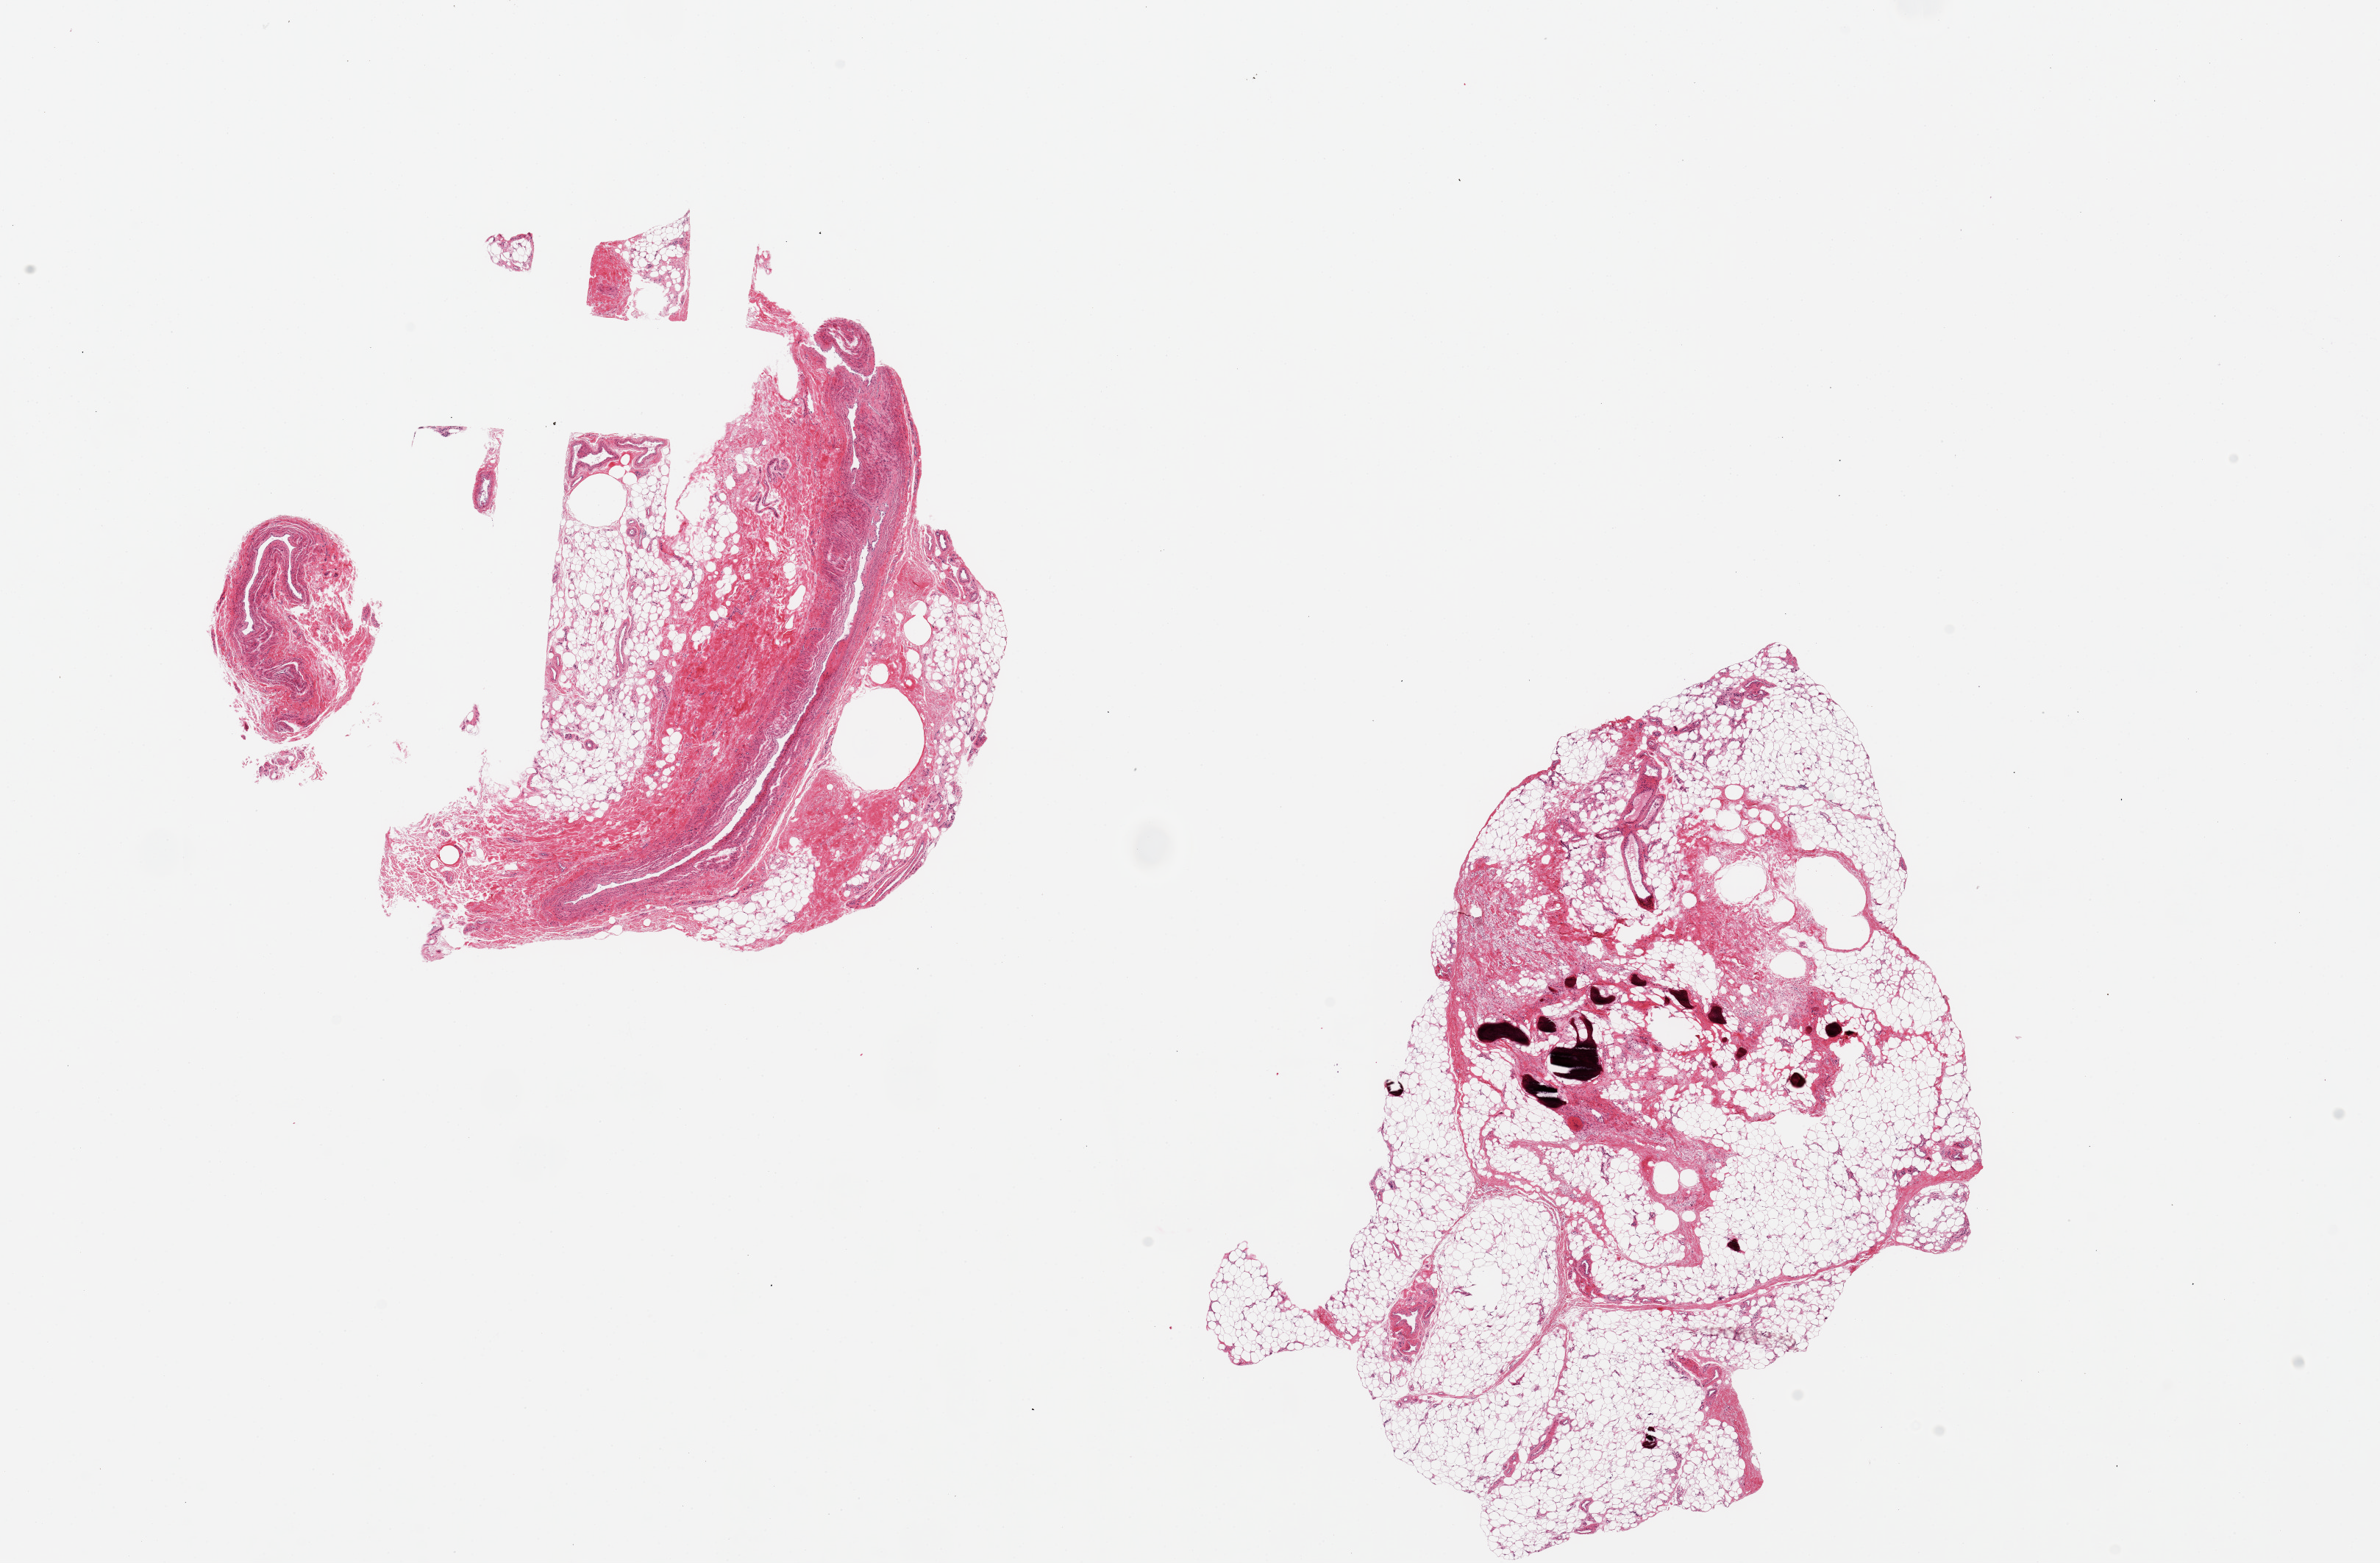
Haematoxylin and eosin whole-slide image — shown as a low-resolution overview of the whole scanned area (about 25.6 x 16.8 mm); PAXgene-fixed, paraffin-embedded tissue; sampled site (target tissue): adipose tissue; tissue donor sample. Donor sex: female.
Pathologist's review note for this sample: 2 pieces, 8.5x8 & 10x7.5mm; 1 piece has focal calcification and possible ossification; other has 50% blood vessels.